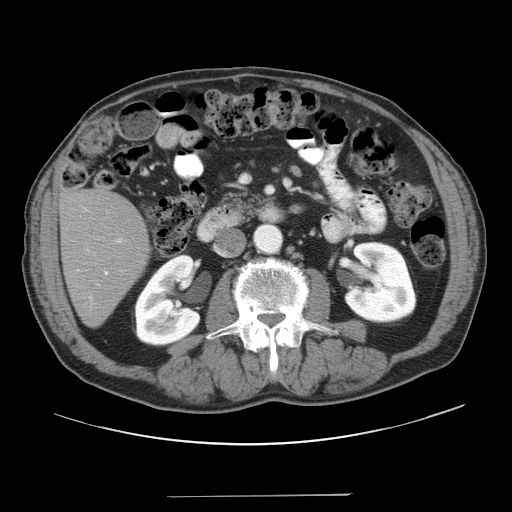
Contrast-enhanced abdominal CT, one axial slice; position 9 of 41 along the scan axis; reconstruction kernel STANDARD; intravenous contrast given; soft-tissue window (W 400 / L 40 HU); 5 mm slice thickness; 512 × 512 image matrix, field of view 420 × 420 mm. Male patient, age 75 years. From the clinical record (not read from this slice): diagnosis: colorectal cancer liver metastases, imaged before liver resection; multiple liver metastases: no; largest metastasis: 5.2 cm; disease in both lobes: no.
Annotated regions visible in this slice (expert manual segmentation):
- liver: bounding box (x1, y1, x2, y2) in pixels: (61, 190, 149, 326)
- planned liver remnant (the part of the liver to remain after resection): (61, 190, 149, 325)
- portal vein (with intrahepatic branches): (97, 238, 123, 285)